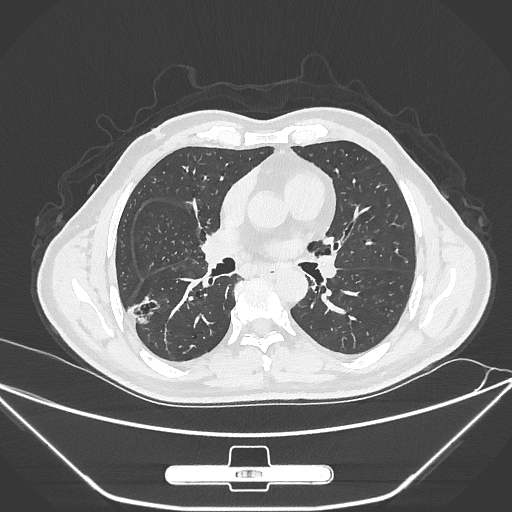
Chest CT, one axial slice. Position 152 of 310 along the scan axis. 120 kVp. Lung window (W 1500 / L -600 HU). 1 mm slice thickness. 512 × 512 image matrix, field of view 398 × 398 mm. Male patient, age 71 years. From the clinical record (not read from this slice): clinical TNM (as recorded): T1c N0 M0; histopathological grade: G2.
Outlined on this slice (rectangle marked by the reading radiologist):
- lung tumour (recorded histology: adenocarcinoma): box from (x=128, y=293) to (x=164, y=330) px